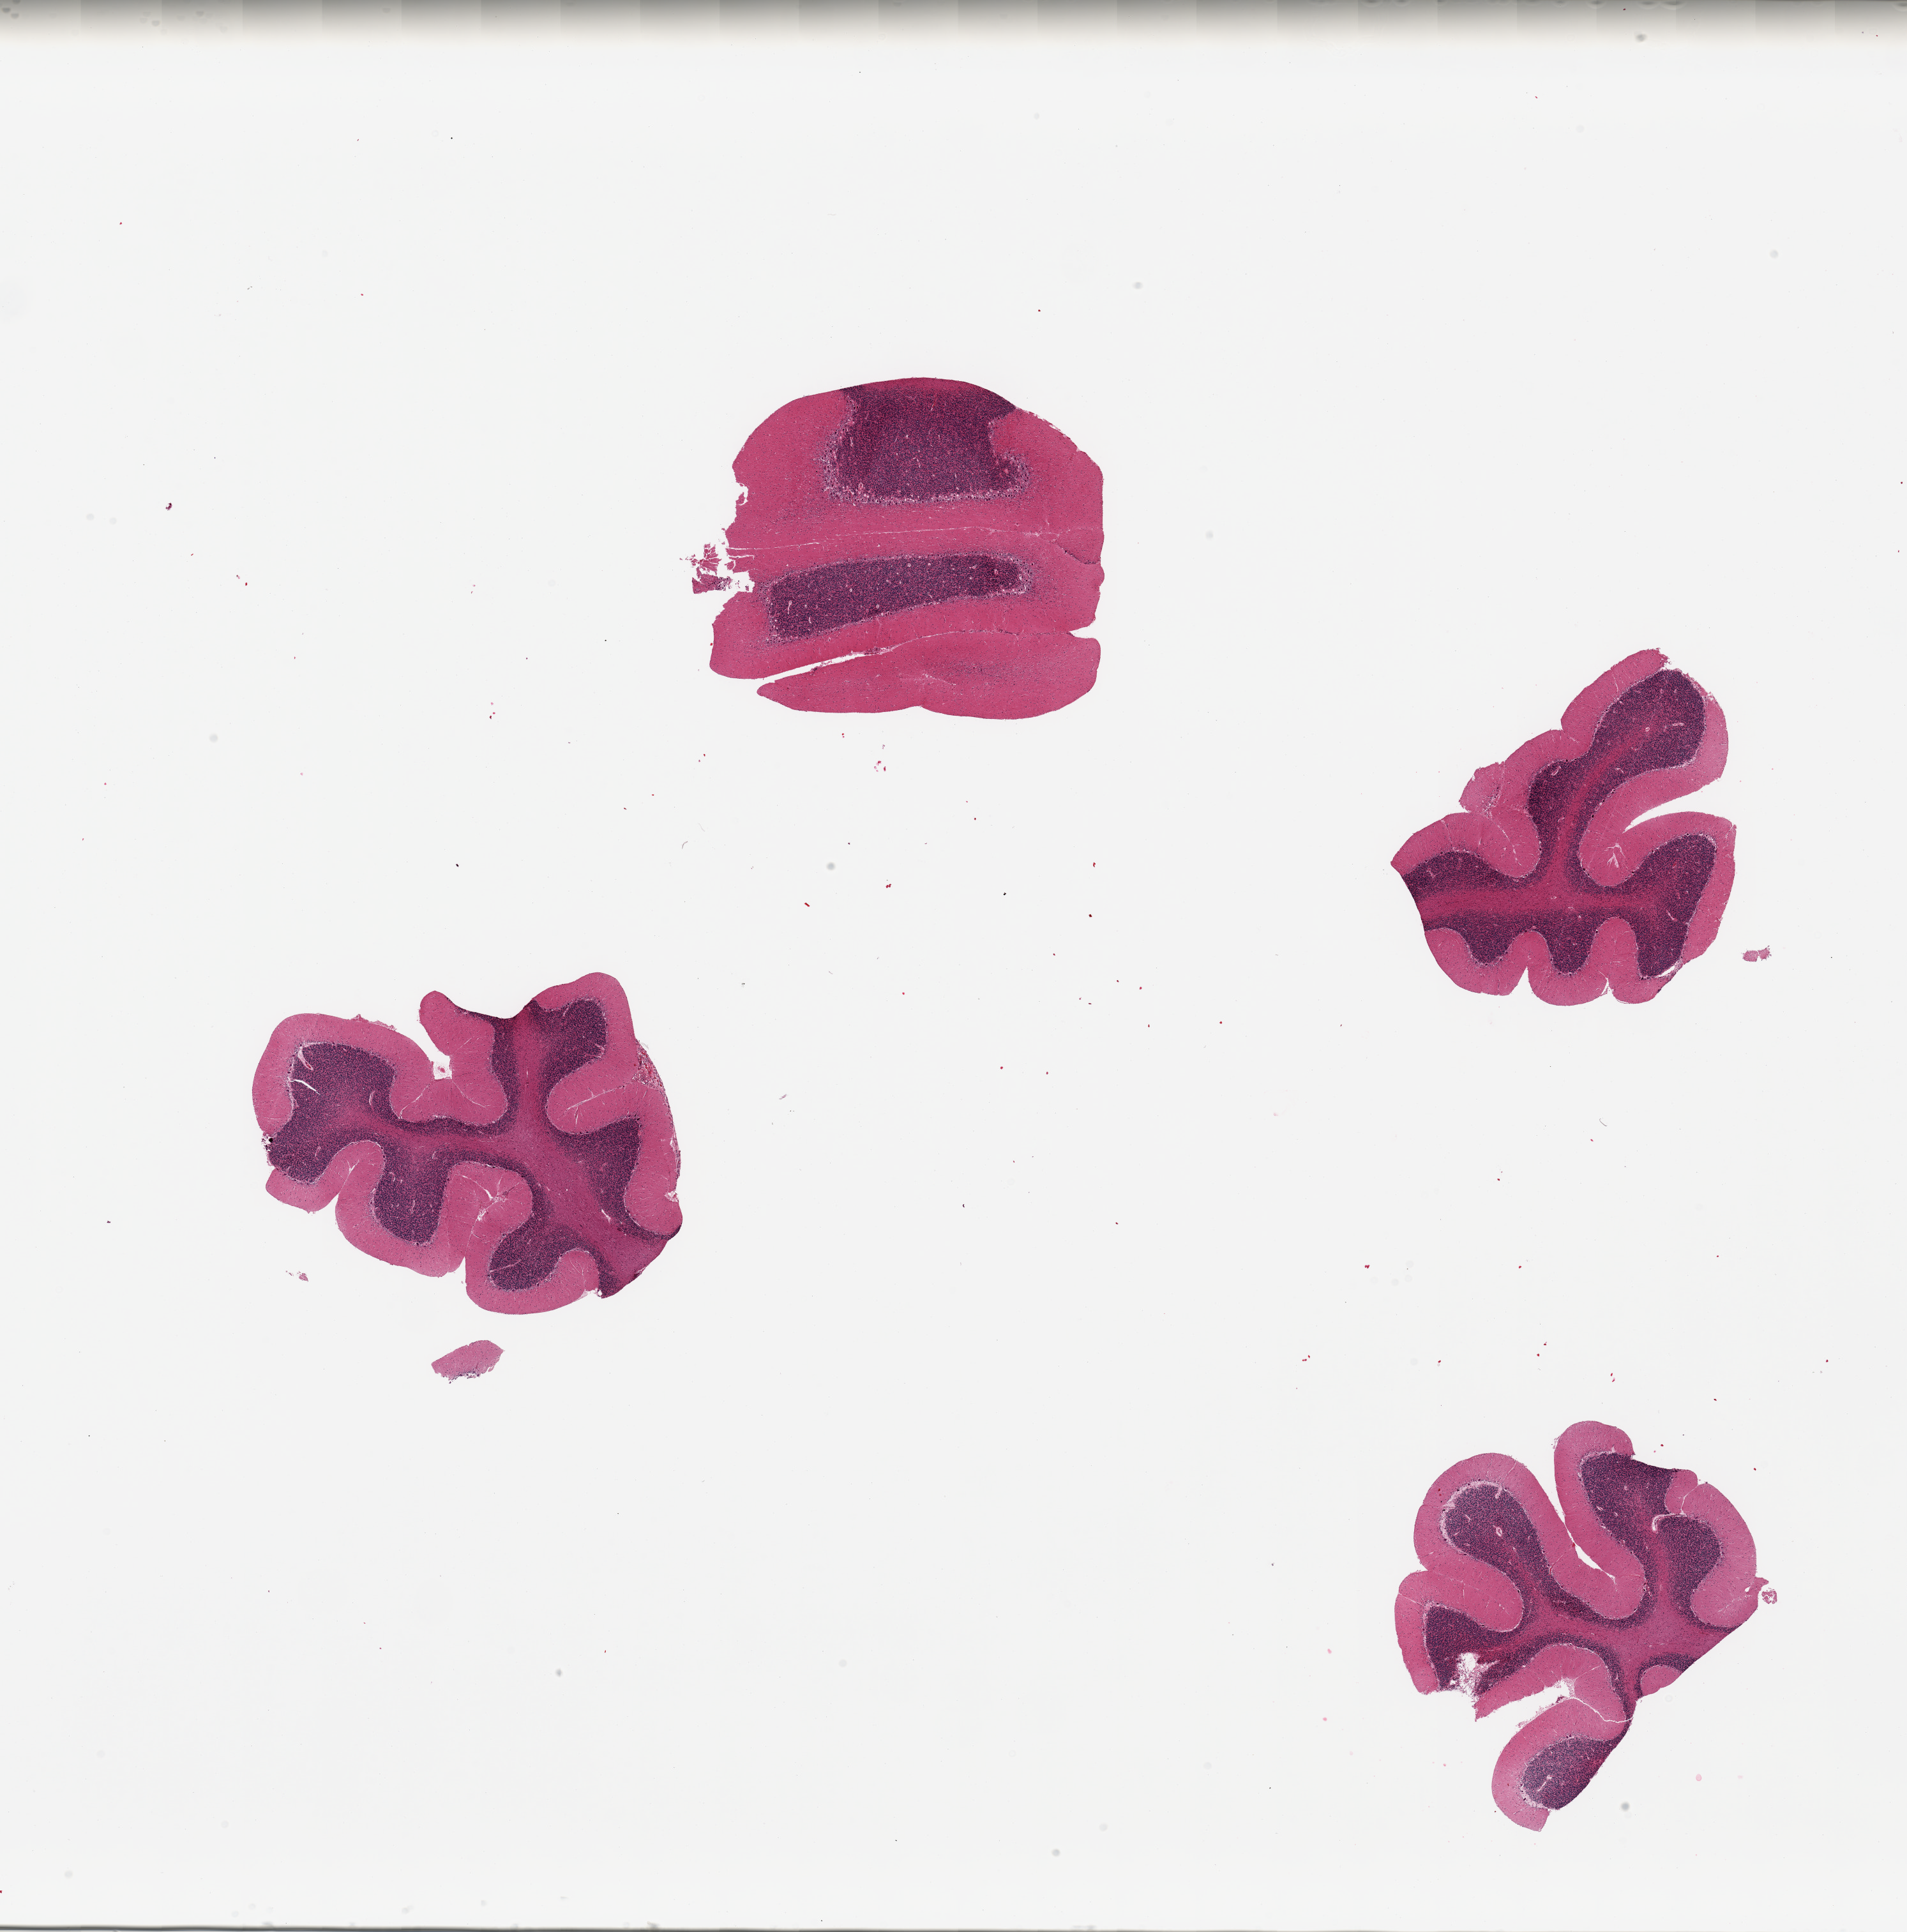
Digitized hematoxylin and eosin (H&E)-stained section, whole scanned area (about 23.6 x 23.9 mm, from a 20x scan) shown as a low-resolution overview, PAXgene-fixed, paraffin-embedded tissue, target tissue: cerebellum, donor tissue sample. Male donor.
• pathologist's review note for this sample: 4 pieces